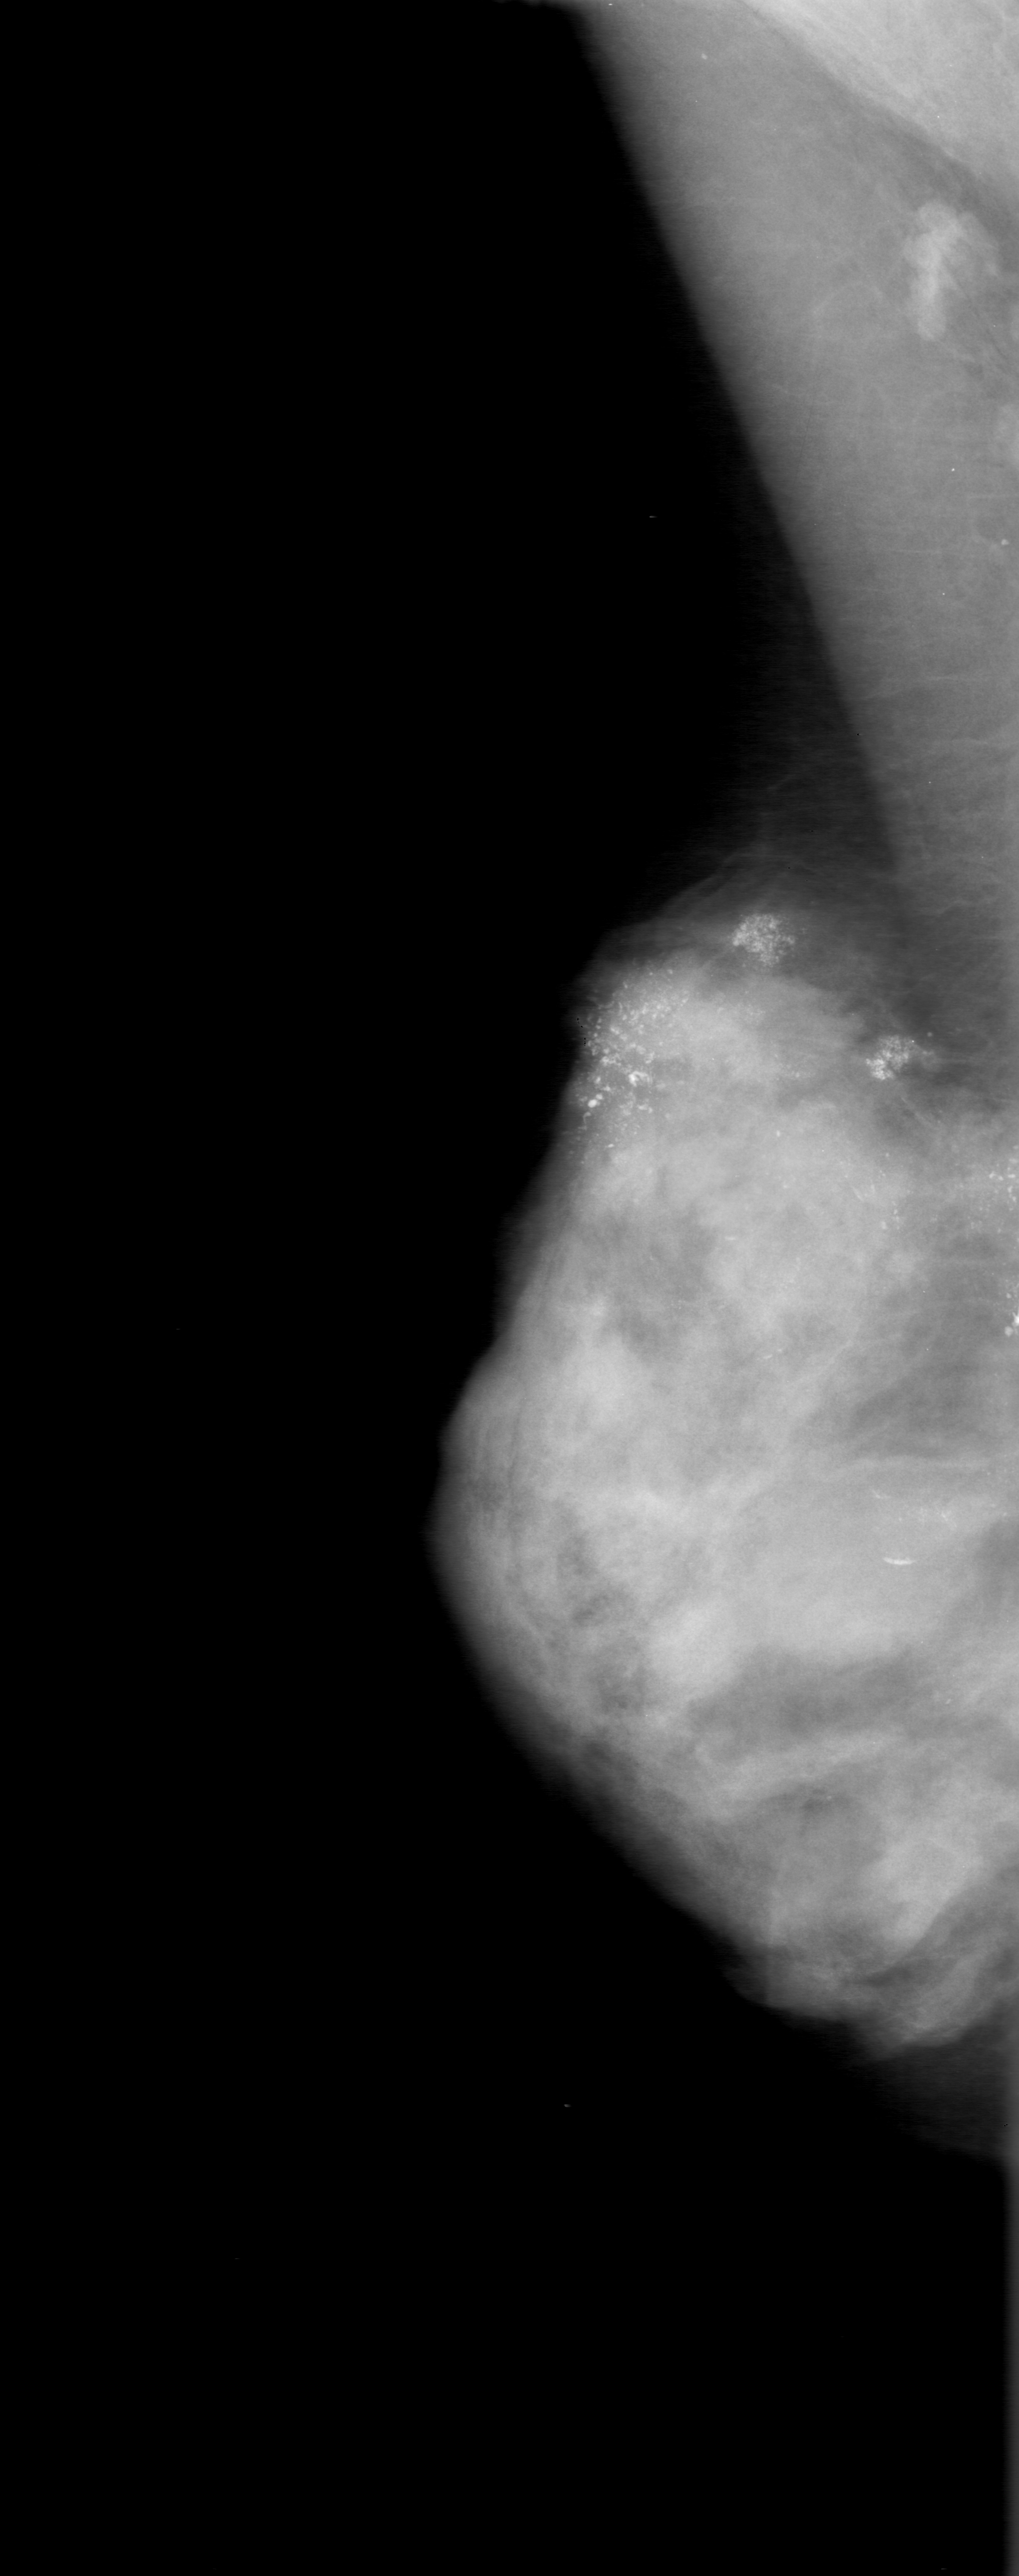
Scanned film-screen mammogram, right breast, mediolateral oblique (MLO) view, BI-RADS breast density category 4 (scale 1–4).
- Marked findings (only marked abnormalities are described; nothing is implied about the rest of the image): calcifications, morphology pleomorphic, distribution segmental; BI-RADS assessment category 5; subtlety rating 5 on a 1 (subtle) to 5 (obvious) scale; pathology (as recorded): malignant.